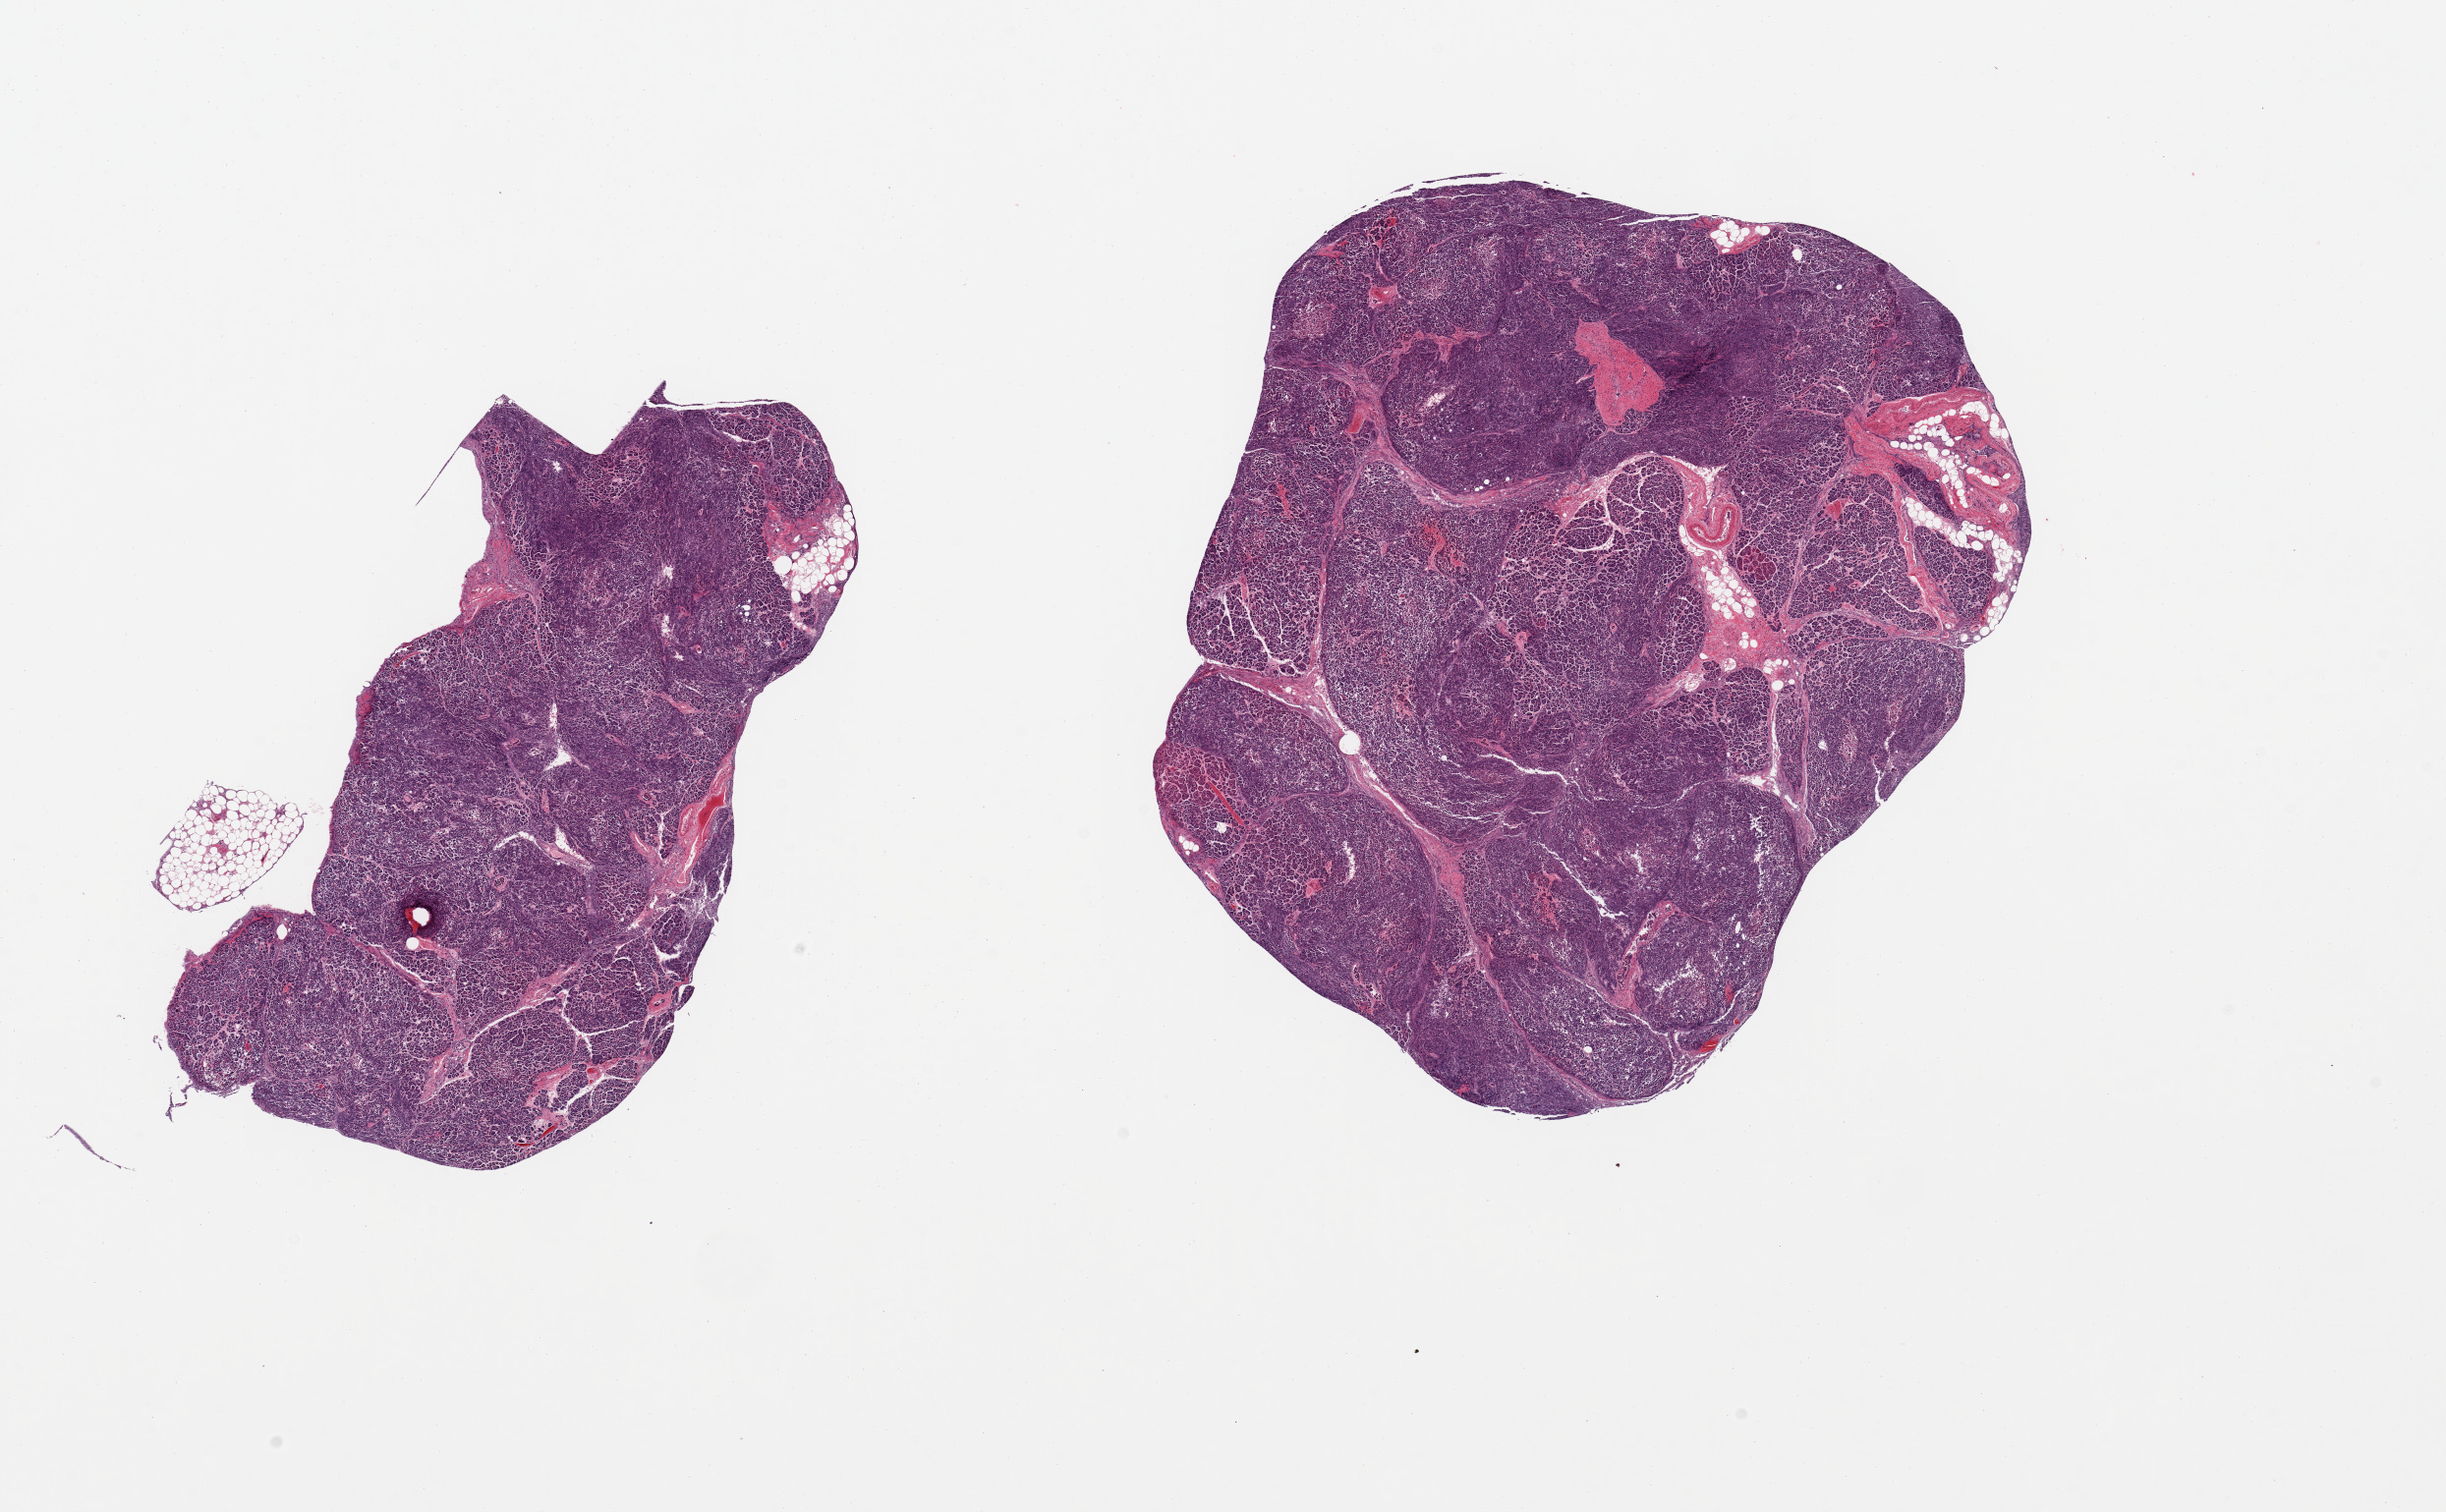
H&E whole-slide image, a low-resolution overview of the entire scanned area, about 19.7 x 12.2 mm (acquisition: 20x scan). PAXgene-fixed, paraffin-embedded tissue. Section of pancreas (target tissue). Donor tissue sample. Donor sex: male.
- pathologist's review note for this sample: 2 pieces